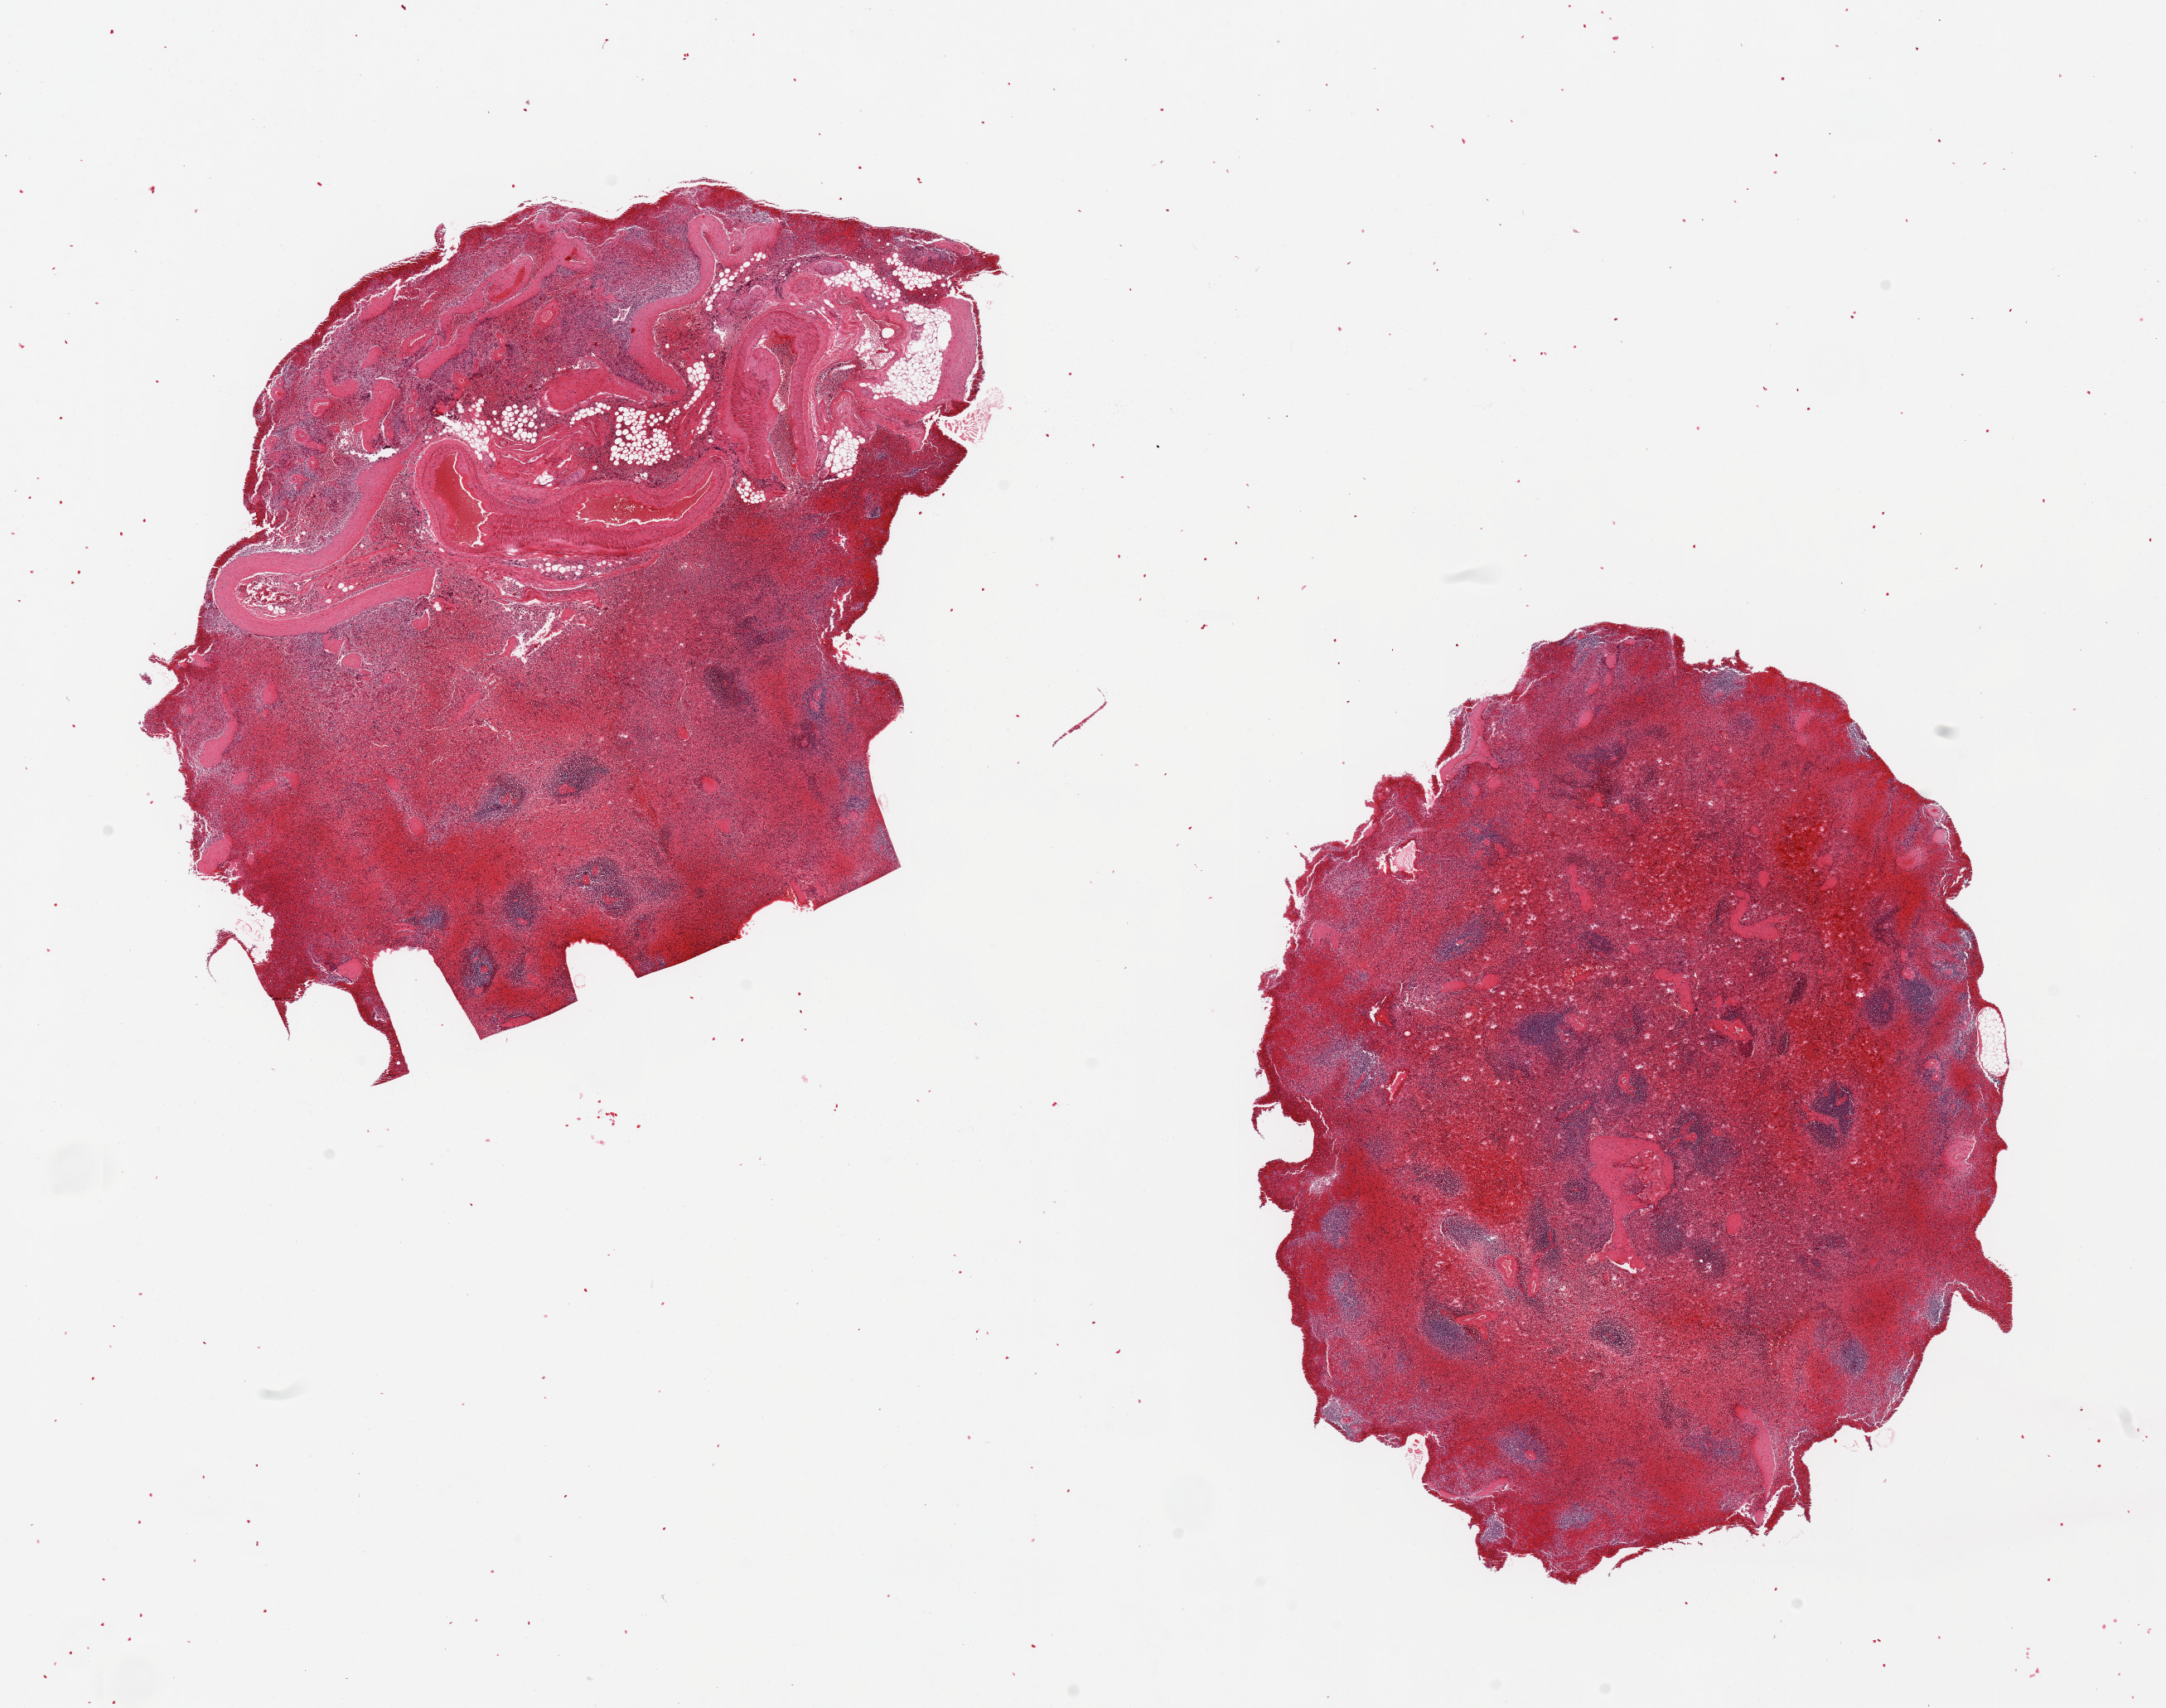
Whole-slide image, haematoxylin and eosin stain, brightfield, a low-resolution overview of the entire scanned area, about 20.7 x 16.3 mm, PAXgene-fixed, paraffin-embedded tissue, target tissue: spleen, donor tissue sample. Donor sex: female.
Reviewer comment on this tissue sample: 2 pieces; congestion, one with large vessle and internal fat up to 30%.